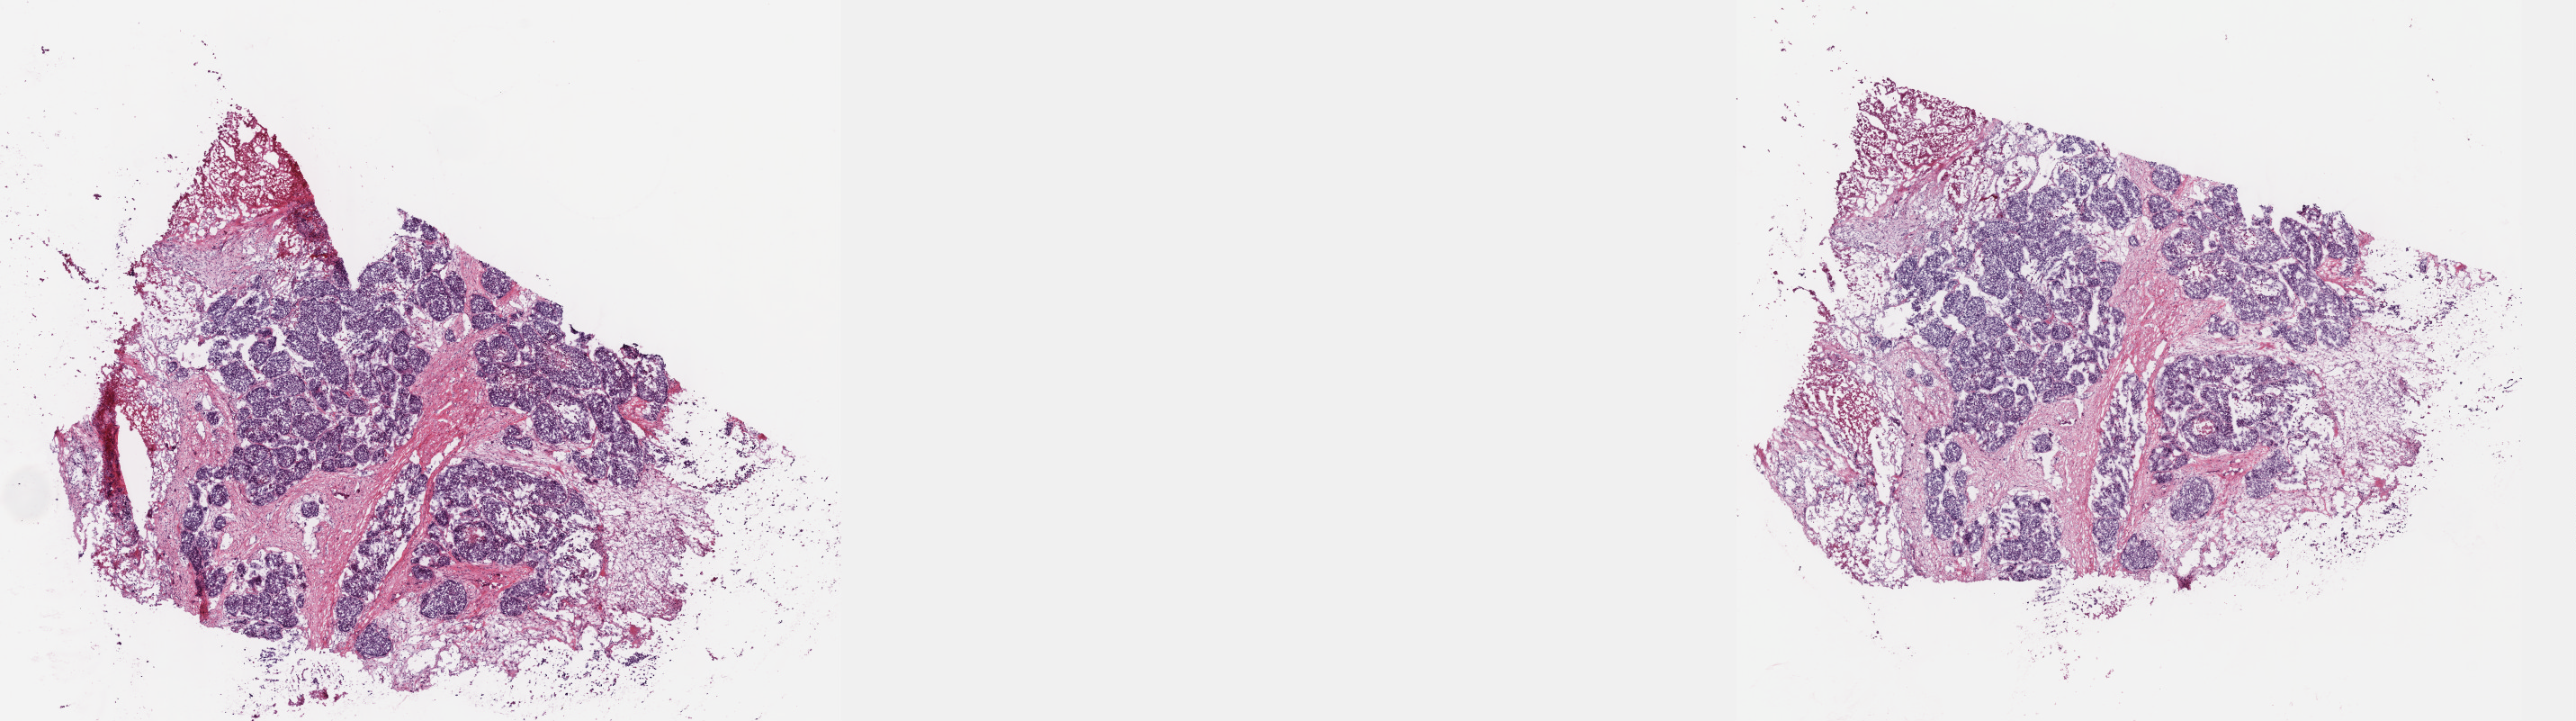
Digitized H&E-stained tissue section (whole slide), a low-resolution overview of the entire scanned area, about 23.1 x 6.5 mm (slide scanned at 40x); frozen section from the top of the tissue portion; sample: primary tumour, liver. Male, age 54 years at initial diagnosis. Histologic grade: G3 (poorly differentiated). Composition of this section per pathologist review: tumour cells 100%, tumour nuclei 60%, normal cells 0%, stromal cells 0%, necrosis 0%. Infiltration values recorded for this section: lymphocyte infiltration 1%, monocyte infiltration 0%, neutrophil infiltration 0%.
AJCC pathologic stage: IIIA (6th edition). Histologic diagnosis: Hepatocellular carcinoma, NOS.